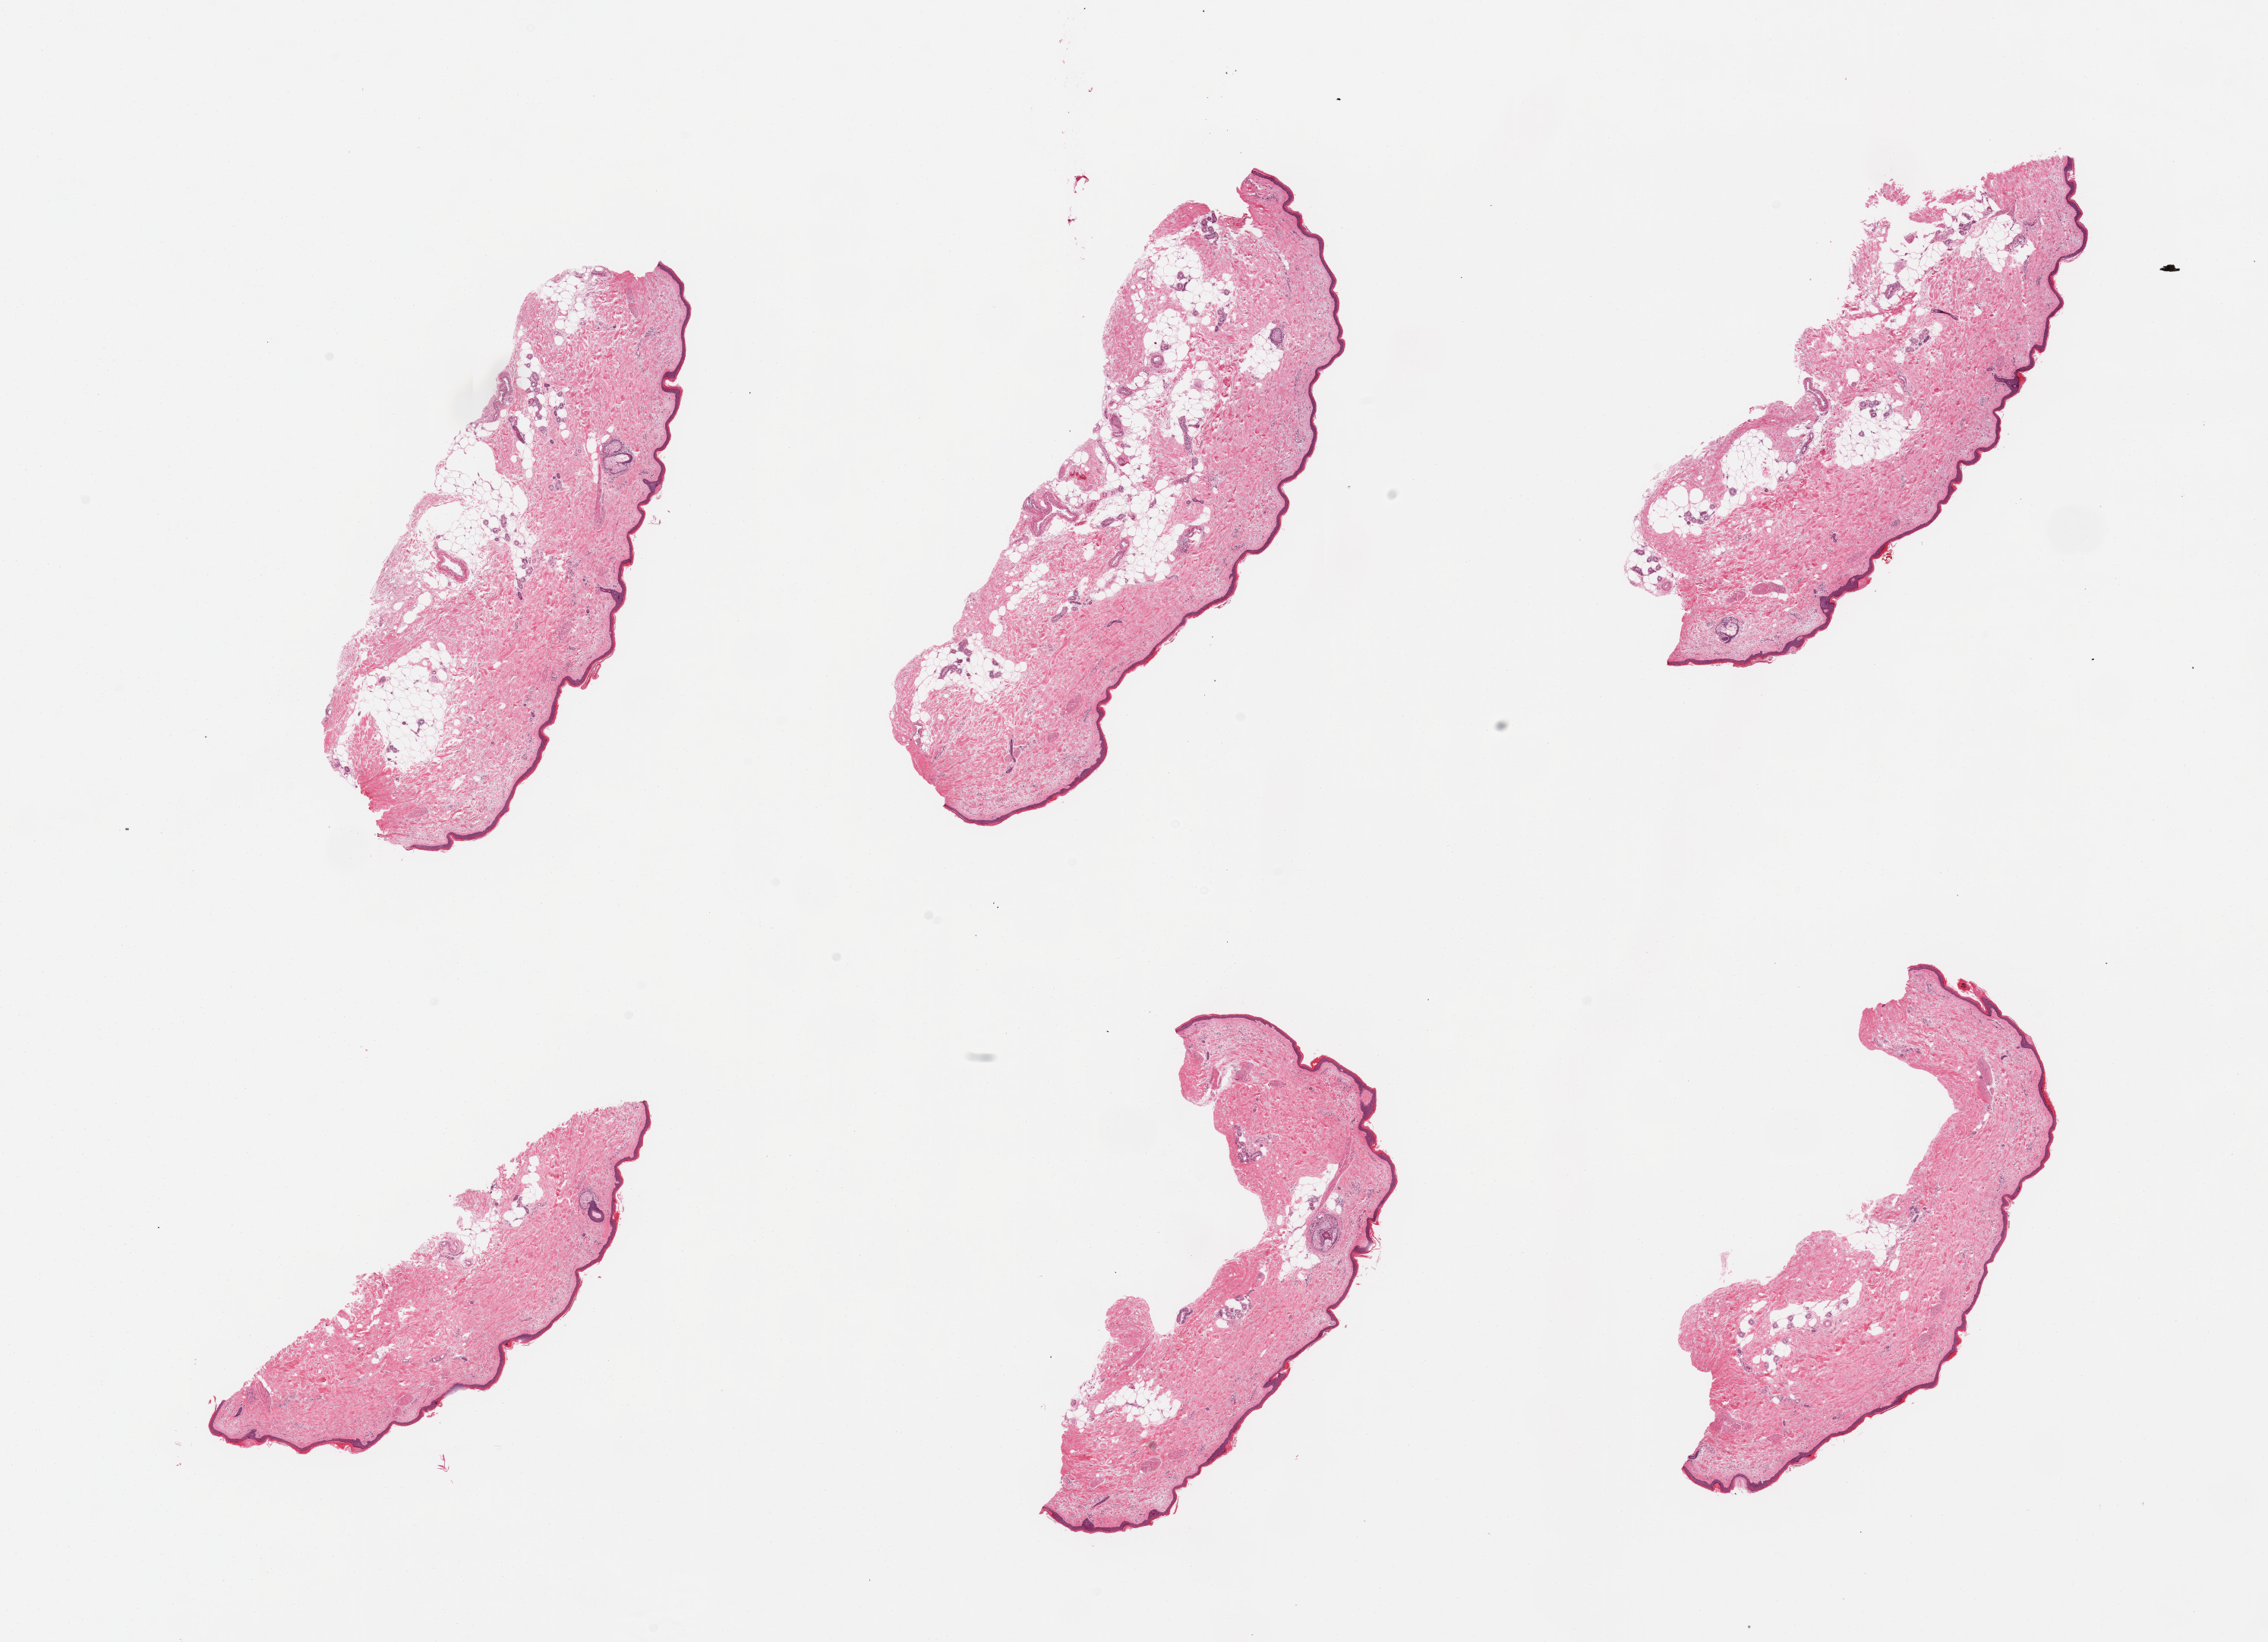
Whole-slide image, haematoxylin and eosin stain, brightfield — a low-resolution overview of the entire scanned area, about 23.6 x 17.1 mm; PAXgene-fixed paraffin-embedded (PFPE) section; sampled site (target tissue): skin of lower leg; donor tissue sample. Donor sex: male.
- pathologist's review note for this sample: 6 pieces, focal adherent fat, nubbins up to ~1mm; Squamous epithelium is ~35-40 microns